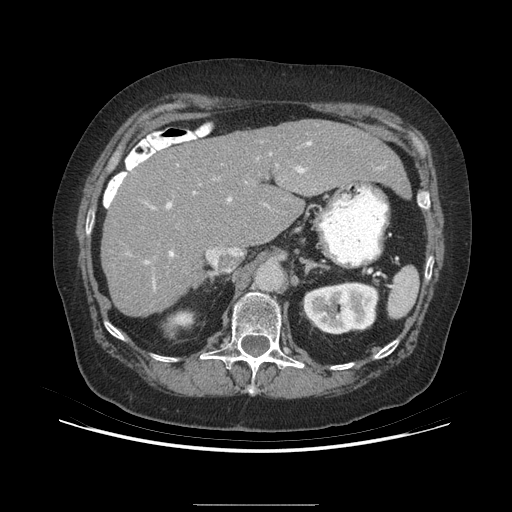
Contrast-enhanced abdominal CT (liver protocol), one axial slice. Slice 158 of 192 in the series (ordered by position). Reconstruction kernel STANDARD. Soft-tissue window (W 400 / L 40 HU). 512 × 512 image matrix, field of view 400 × 400 mm. From the clinical record (not read from this slice): diagnosis: hepatocellular carcinoma (patient treated with transarterial chemoembolisation; whether this scan precedes or follows treatment is not stated here); TNM stage (as recorded): Stage-I; Child-Pugh class: A; tumour differentiation: moderately differentiated; tumour size: 3.2 cm.
Annotated regions visible in this slice (semi-automatically segmented with operator editing):
- liver parenchyma outside the tumour (the mass and vessels are separate outlines, so this box may not span the whole liver): bounding box [x1, y1, x2, y2] px = [100, 120, 406, 316]
- liver vessels: [145, 142, 312, 288]